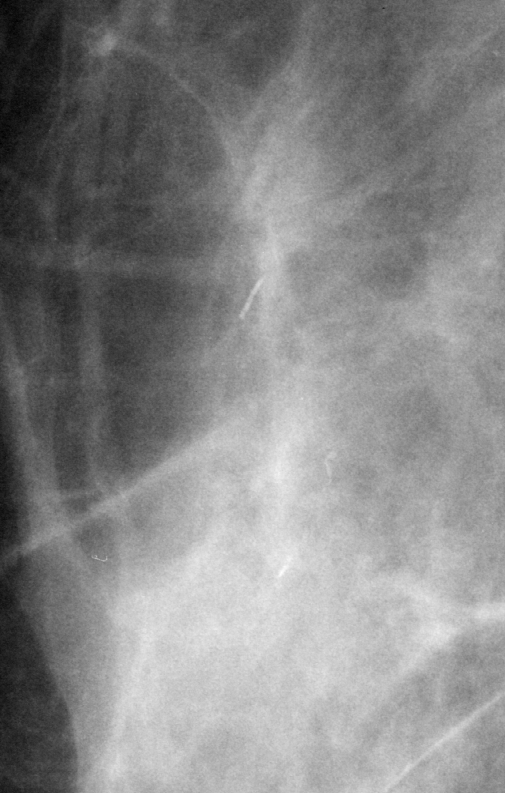
Region of interest cut from a scanned film mammogram (one marked finding), right breast, MLO view, BI-RADS breast density category 2 (scale 1–4).
Finding: calcifications, morphology fine linear branching, distribution linear; BI-RADS assessment category 4; subtlety rating 4 on a 1 (subtle) to 5 (obvious) scale; pathology (as recorded): benign.